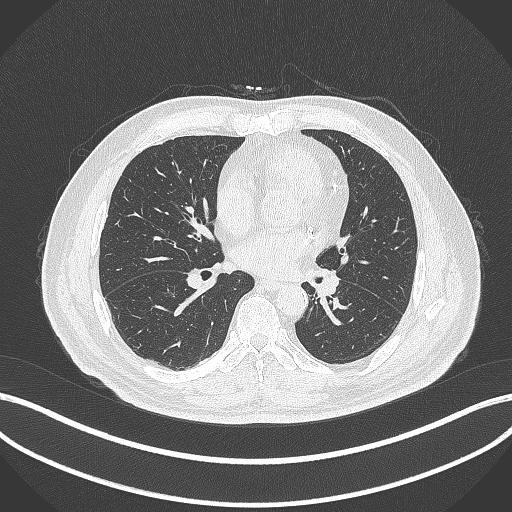
Chest CT, one axial slice. Slice 131 of 312 in the series (ordered by position). Reconstruction kernel B70f. 120 kVp. Lung window (W 1500 / L -600 HU). 1 mm slice thickness. 512 × 512 image matrix, field of view 400 × 400 mm. Male patient, age 71 years. Case-level facts recorded for this patient, not image findings: clinical TNM (as recorded): T1b N0 M0.
Structures marked on this image (rectangle marked by the reading radiologist):
- lung tumour (recorded histology: squamous cell carcinoma): bounding box (x1, y1, x2, y2) in pixels: (316, 268, 342, 298)